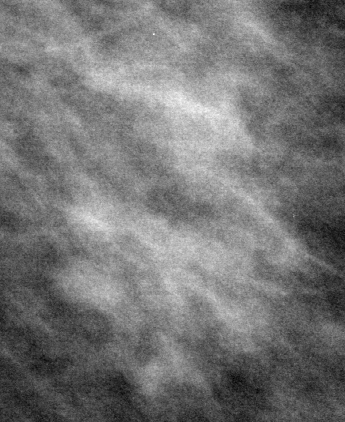
Crop from a digitized film mammogram around one marked abnormality; left breast; MLO view; BI-RADS breast density category 1 (scale 1–4).
Marked abnormality: mass, shape lobulated, margins ill defined; BI-RADS assessment category 4; subtlety rating 4 on a 1 (subtle) to 5 (obvious) scale; pathology result (as recorded, not read from the image): malignant.